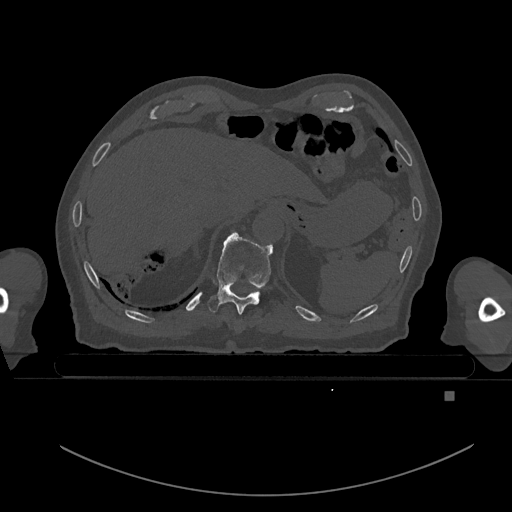
CT including the spine, one axial slice. Slice 86 of 969 in the series (ordered by position). Bone window (W 1800 / L 400 HU). 0.5 mm slice thickness. 512 × 512 image matrix, field of view 456 × 456 mm. Male patient, age 82 years. From the clinical record (not read from this slice): primary cancer: prostate.
Outlined on this slice (semi-automatically segmented with operator editing):
- T10 vertebra: bounding box (x1, y1, x2, y2) in pixels: (208, 233, 273, 314)